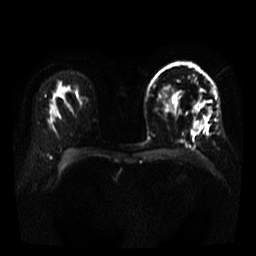
Breast MRI, one axial slice. Position 24 of 35 along the scan axis. Diffusion-weighted series; image 2 of 4 stored at this slice position (different b-values; order by instance number). 3 T. 5 mm slice thickness. 256 × 256 image matrix. Female patient.
Annotated regions visible in this slice (expert manual segmentation):
- tumour on diffusion-weighted imaging: bounding box <193,124,199,132> (left, top, right, bottom; pixels)